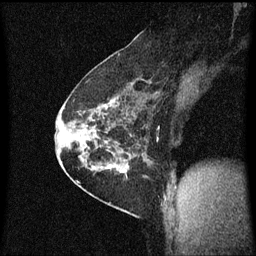
Breast MRI (dynamic contrast-enhanced), one sagittal slice. Dynamic contrast-enhanced series, image 2 of 3 at this slice position (ordered by acquisition). 1.5 T. TE 4.2 ms, TR 8.4 ms. 2 mm slice thickness. 256 × 256 image matrix. Female patient, age 60 years.
Outlined on this slice (semi-automatic segmentation, software-assisted and operator-edited):
- analysis volume of interest (the breast-tissue region the enhancement analysis was run in; not a lesion): box from (x=69, y=66) to (x=149, y=193) px
- tumour enhancement mask (voxels above the 70 % enhancement threshold inside the analysis volume of interest): (x=72, y=84)–(x=149, y=175)